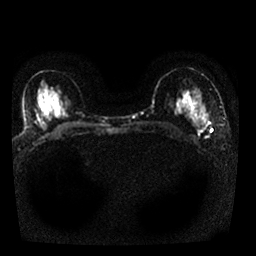
Breast MRI, one axial slice; position 9 of 25 along the scan axis; diffusion-weighted series; image 2 of 4 stored at this slice position (different b-values; order by instance number); 1.5 T; 4 mm slice thickness; 256 × 256 image matrix, field of view 330 × 330 mm. Female patient.
Structures marked on this image (expert manual segmentation):
- tumour on diffusion-weighted imaging: box from (x=199, y=124) to (x=208, y=132) px